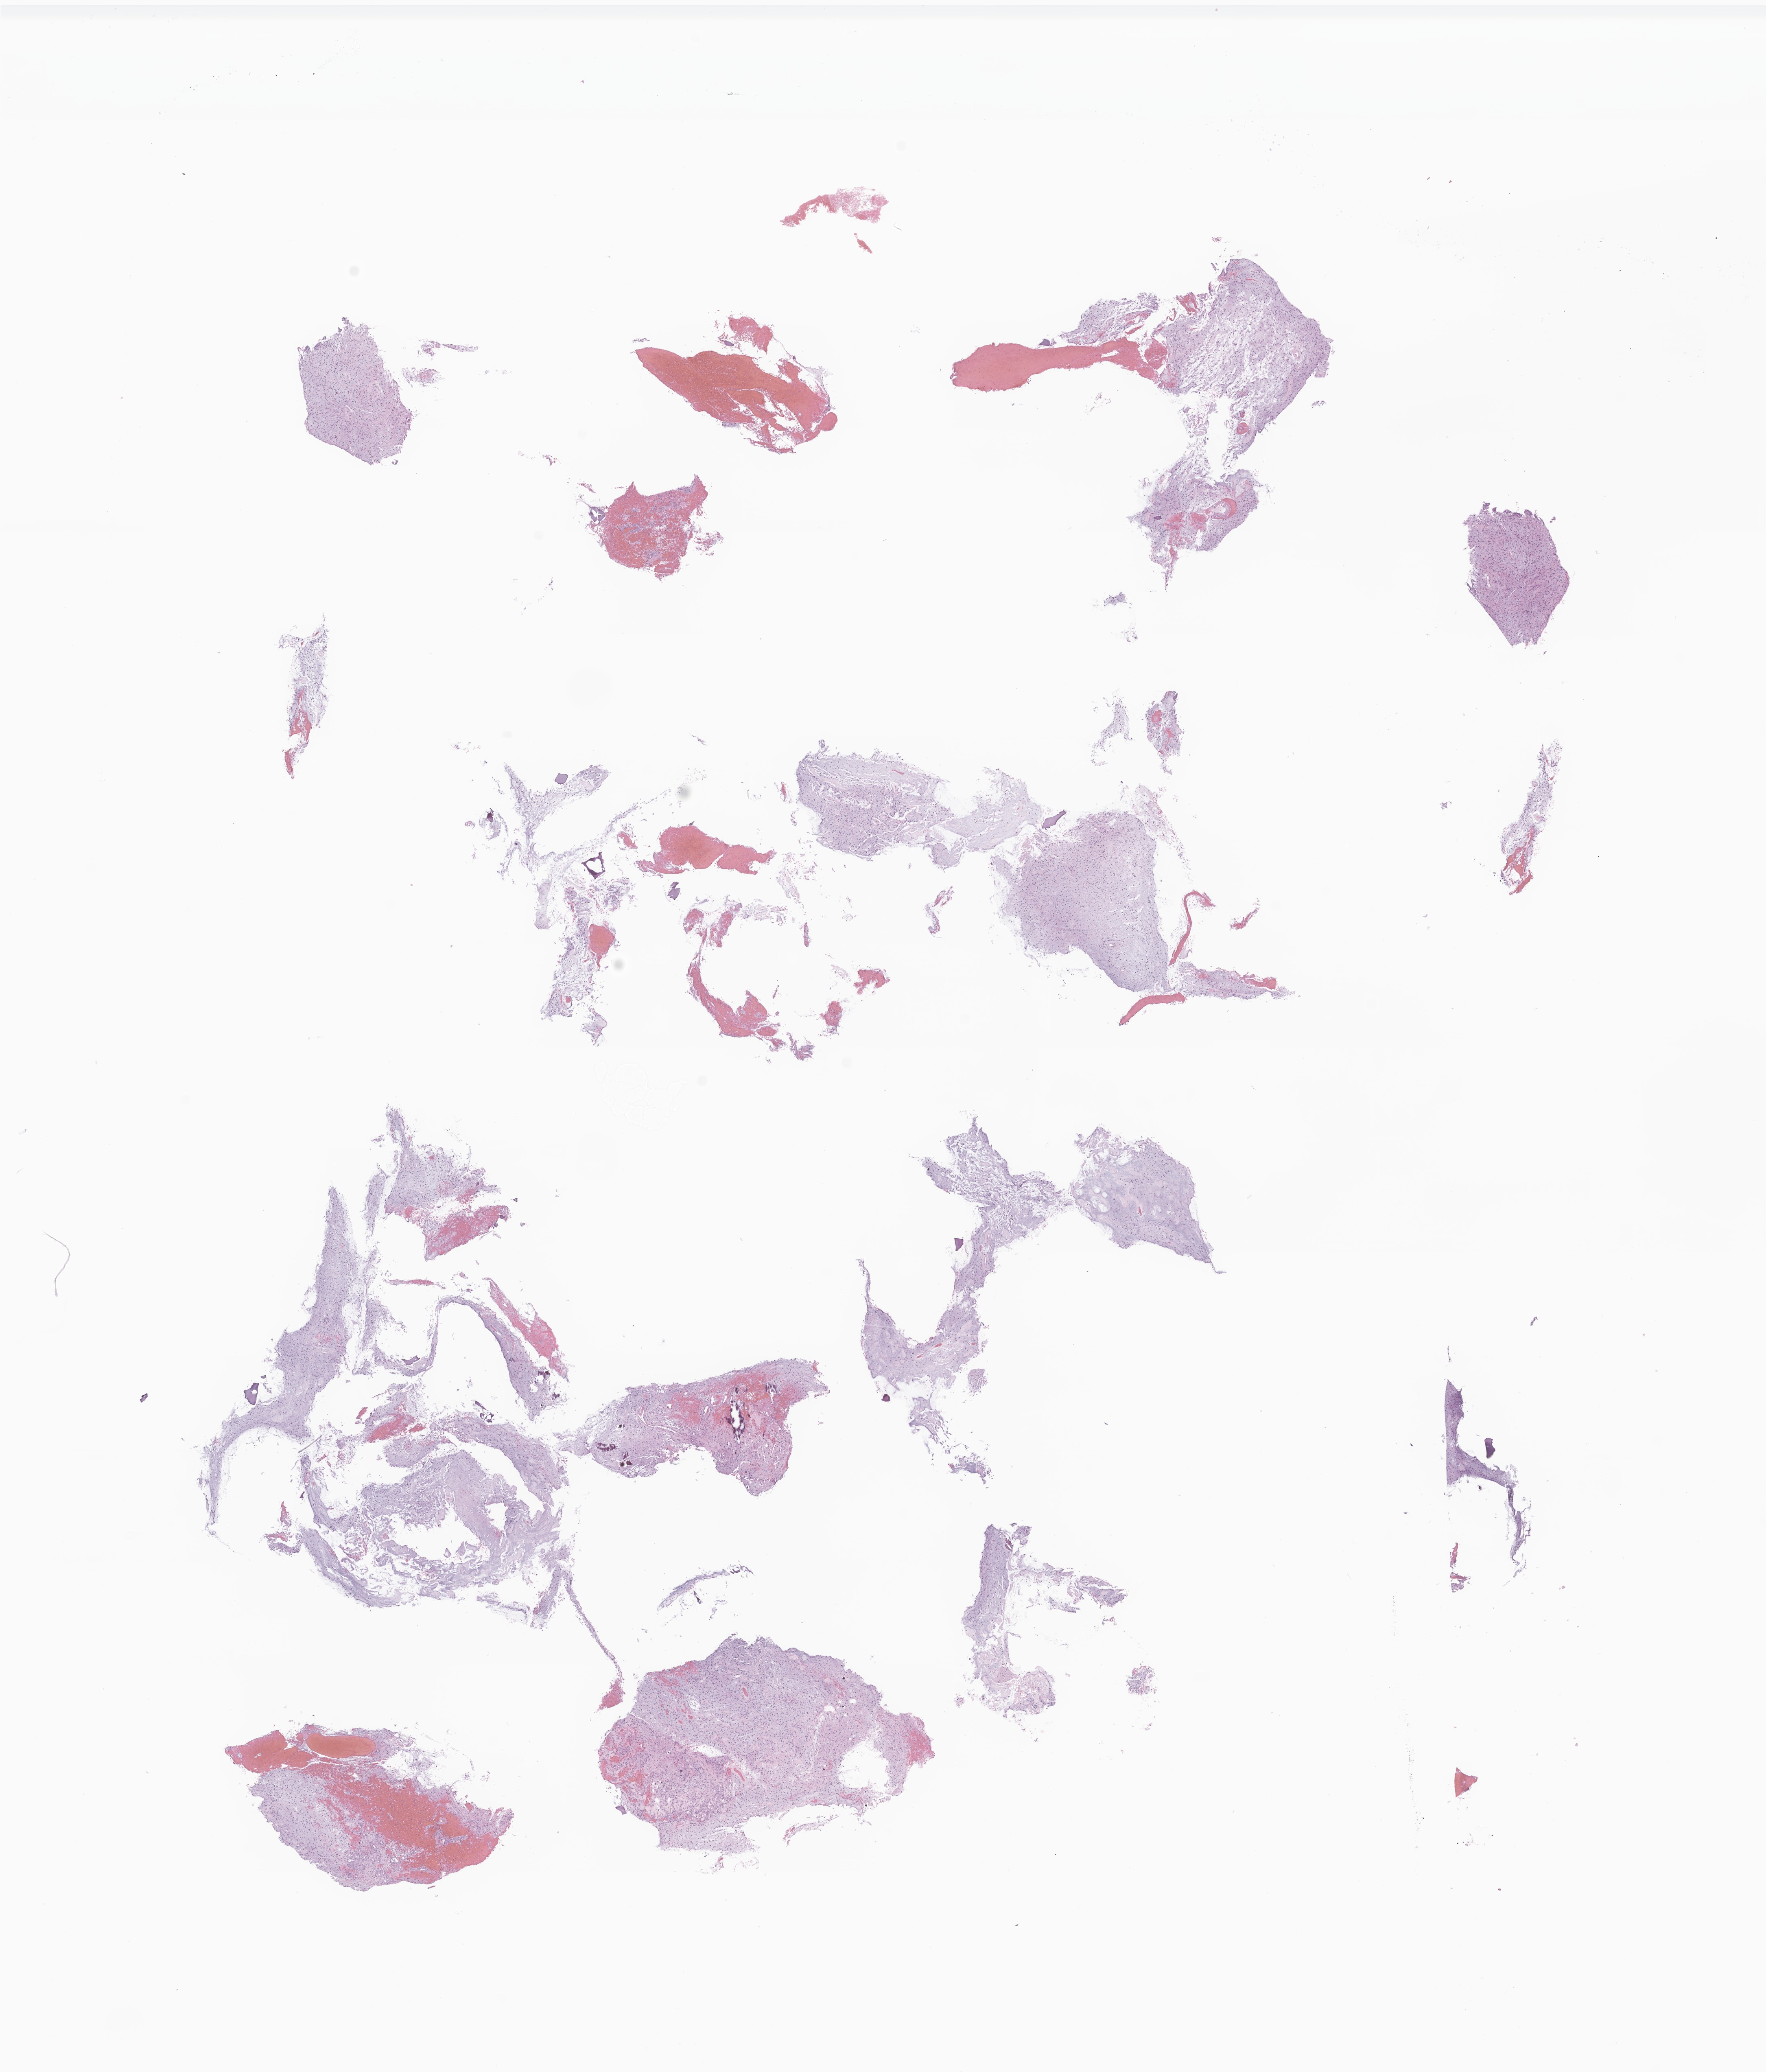
Whole-slide image, hematoxylin and eosin (H&E) stain of tumor tissue from the brain, whole scanned area (about 18.3 x 21.5 mm) shown as a low-resolution overview. FFPE section. Male patient, age 139 months (11 years 7 months).
Diagnosis: Glioma, malignant.